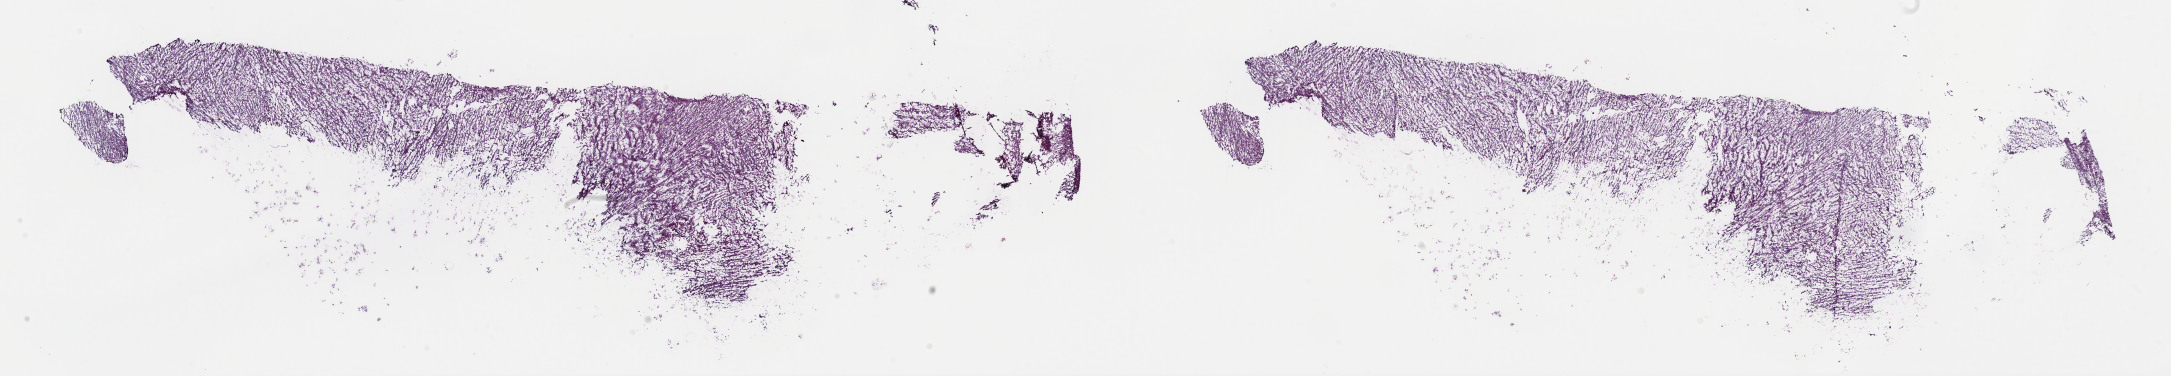
Whole-slide histology image, Hematoxylin and eosin (H&E) stained — low-resolution overview of the scanned area, about 34.3 x 5.9 mm (slide scanned at 40x). Frozen section from the top of the tissue portion. Sample: primary tumour, retroperitoneum and peritoneum. Male patient; age at initial diagnosis 60 years. Slide review estimates, as recorded: tumour cells 99%, tumour nuclei 90%, normal cells 0%, stromal cells 1%, necrosis 0%. Inflammatory infiltration, as recorded: lymphocyte infiltration 0%, monocyte infiltration 0%, neutrophil infiltration 0%.
Diagnosis: Dedifferentiated liposarcoma (retroperitoneum).